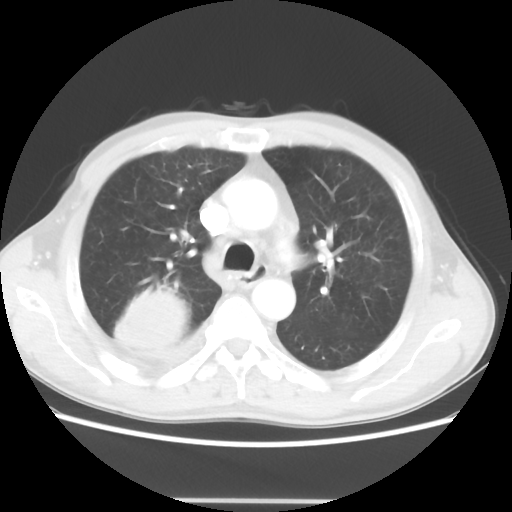
Chest CT, one axial slice; slice 34 of 48 in the series (ordered by position); reconstruction kernel STANDARD; lung window (W 1500 / L -600 HU); 512 × 512 image matrix. Male patient, age 66 years. Case-level facts recorded for this patient, not image findings: clinical TNM (as recorded): T4 N1 M1; histopathological grade: G3.
Structures marked on this image (bounding box drawn by a radiologist):
- lung tumour (recorded histology: small cell carcinoma): box from (x=110, y=283) to (x=187, y=361) px